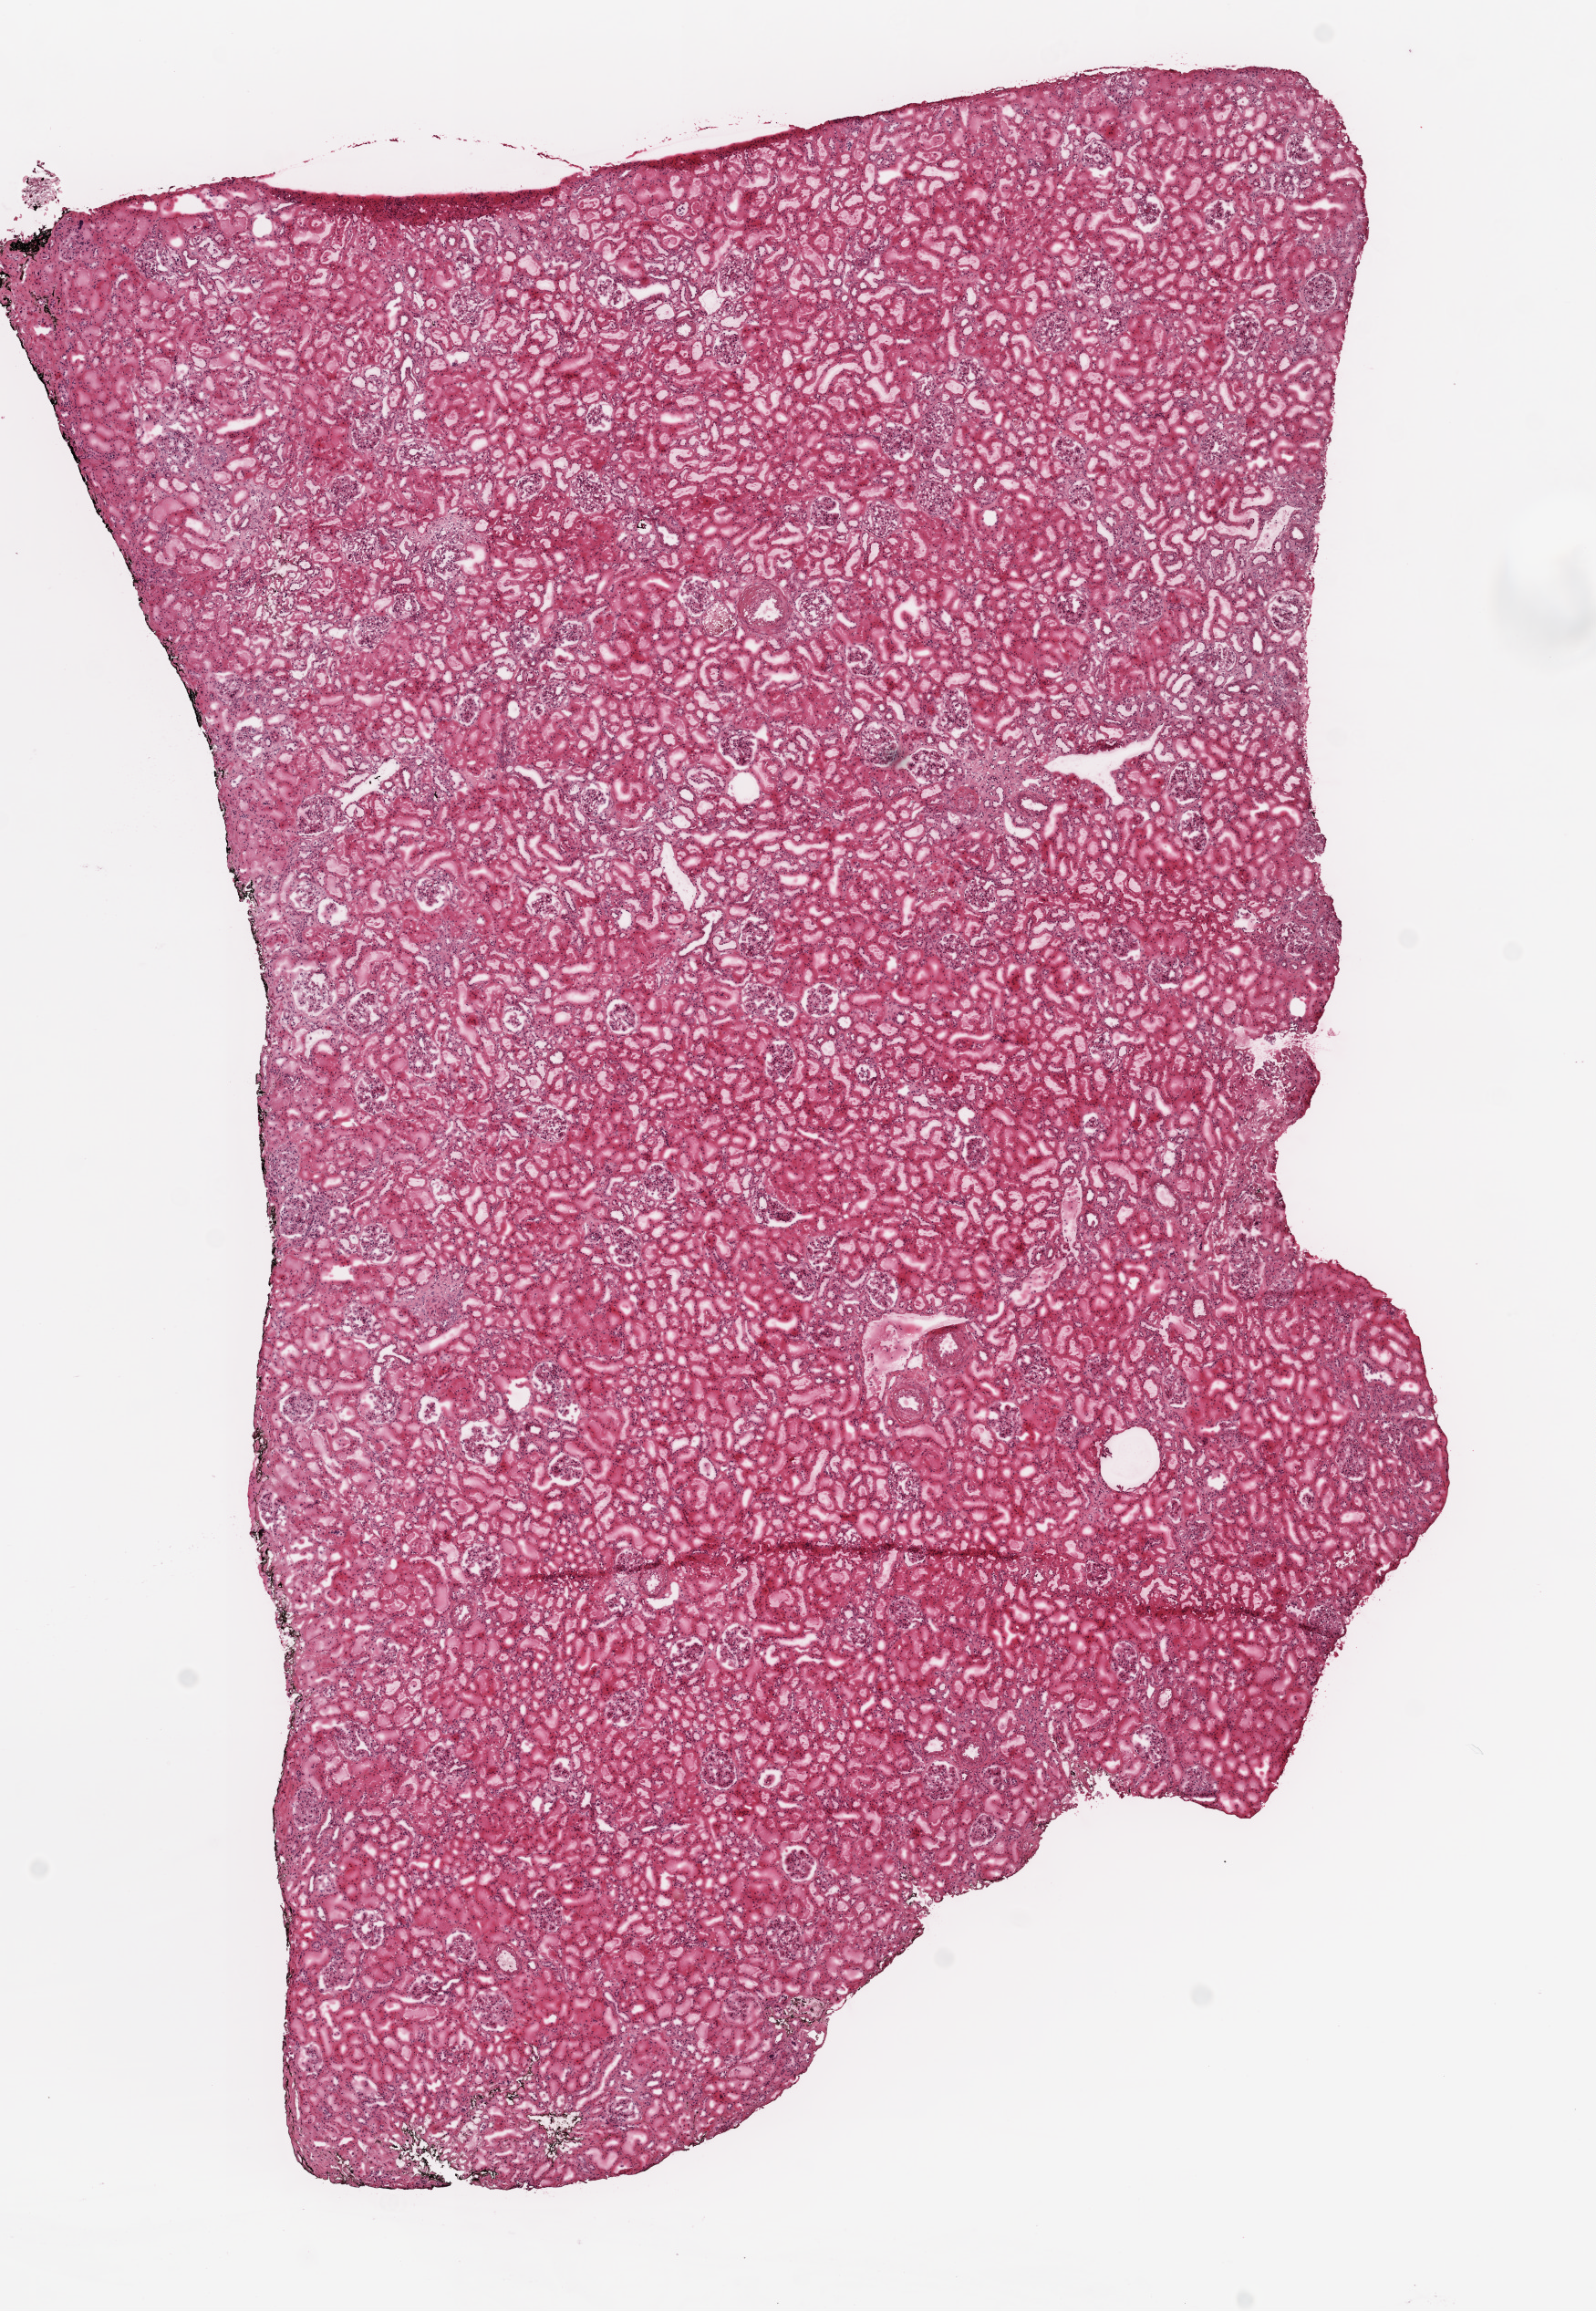
H&E-stained whole-slide image, shown as a low-resolution overview of the whole scanned area (about 7.0 x 10.2 mm). Frozen section from the top of the tissue portion. Solid tissue normal (non-tumour tissue) sample from the kidney. Male patient; age at initial diagnosis 60 years.
This section: solid tissue normal (non-tumour) sample from the same patient. Patient diagnosis: Clear cell adenocarcinoma, NOS.